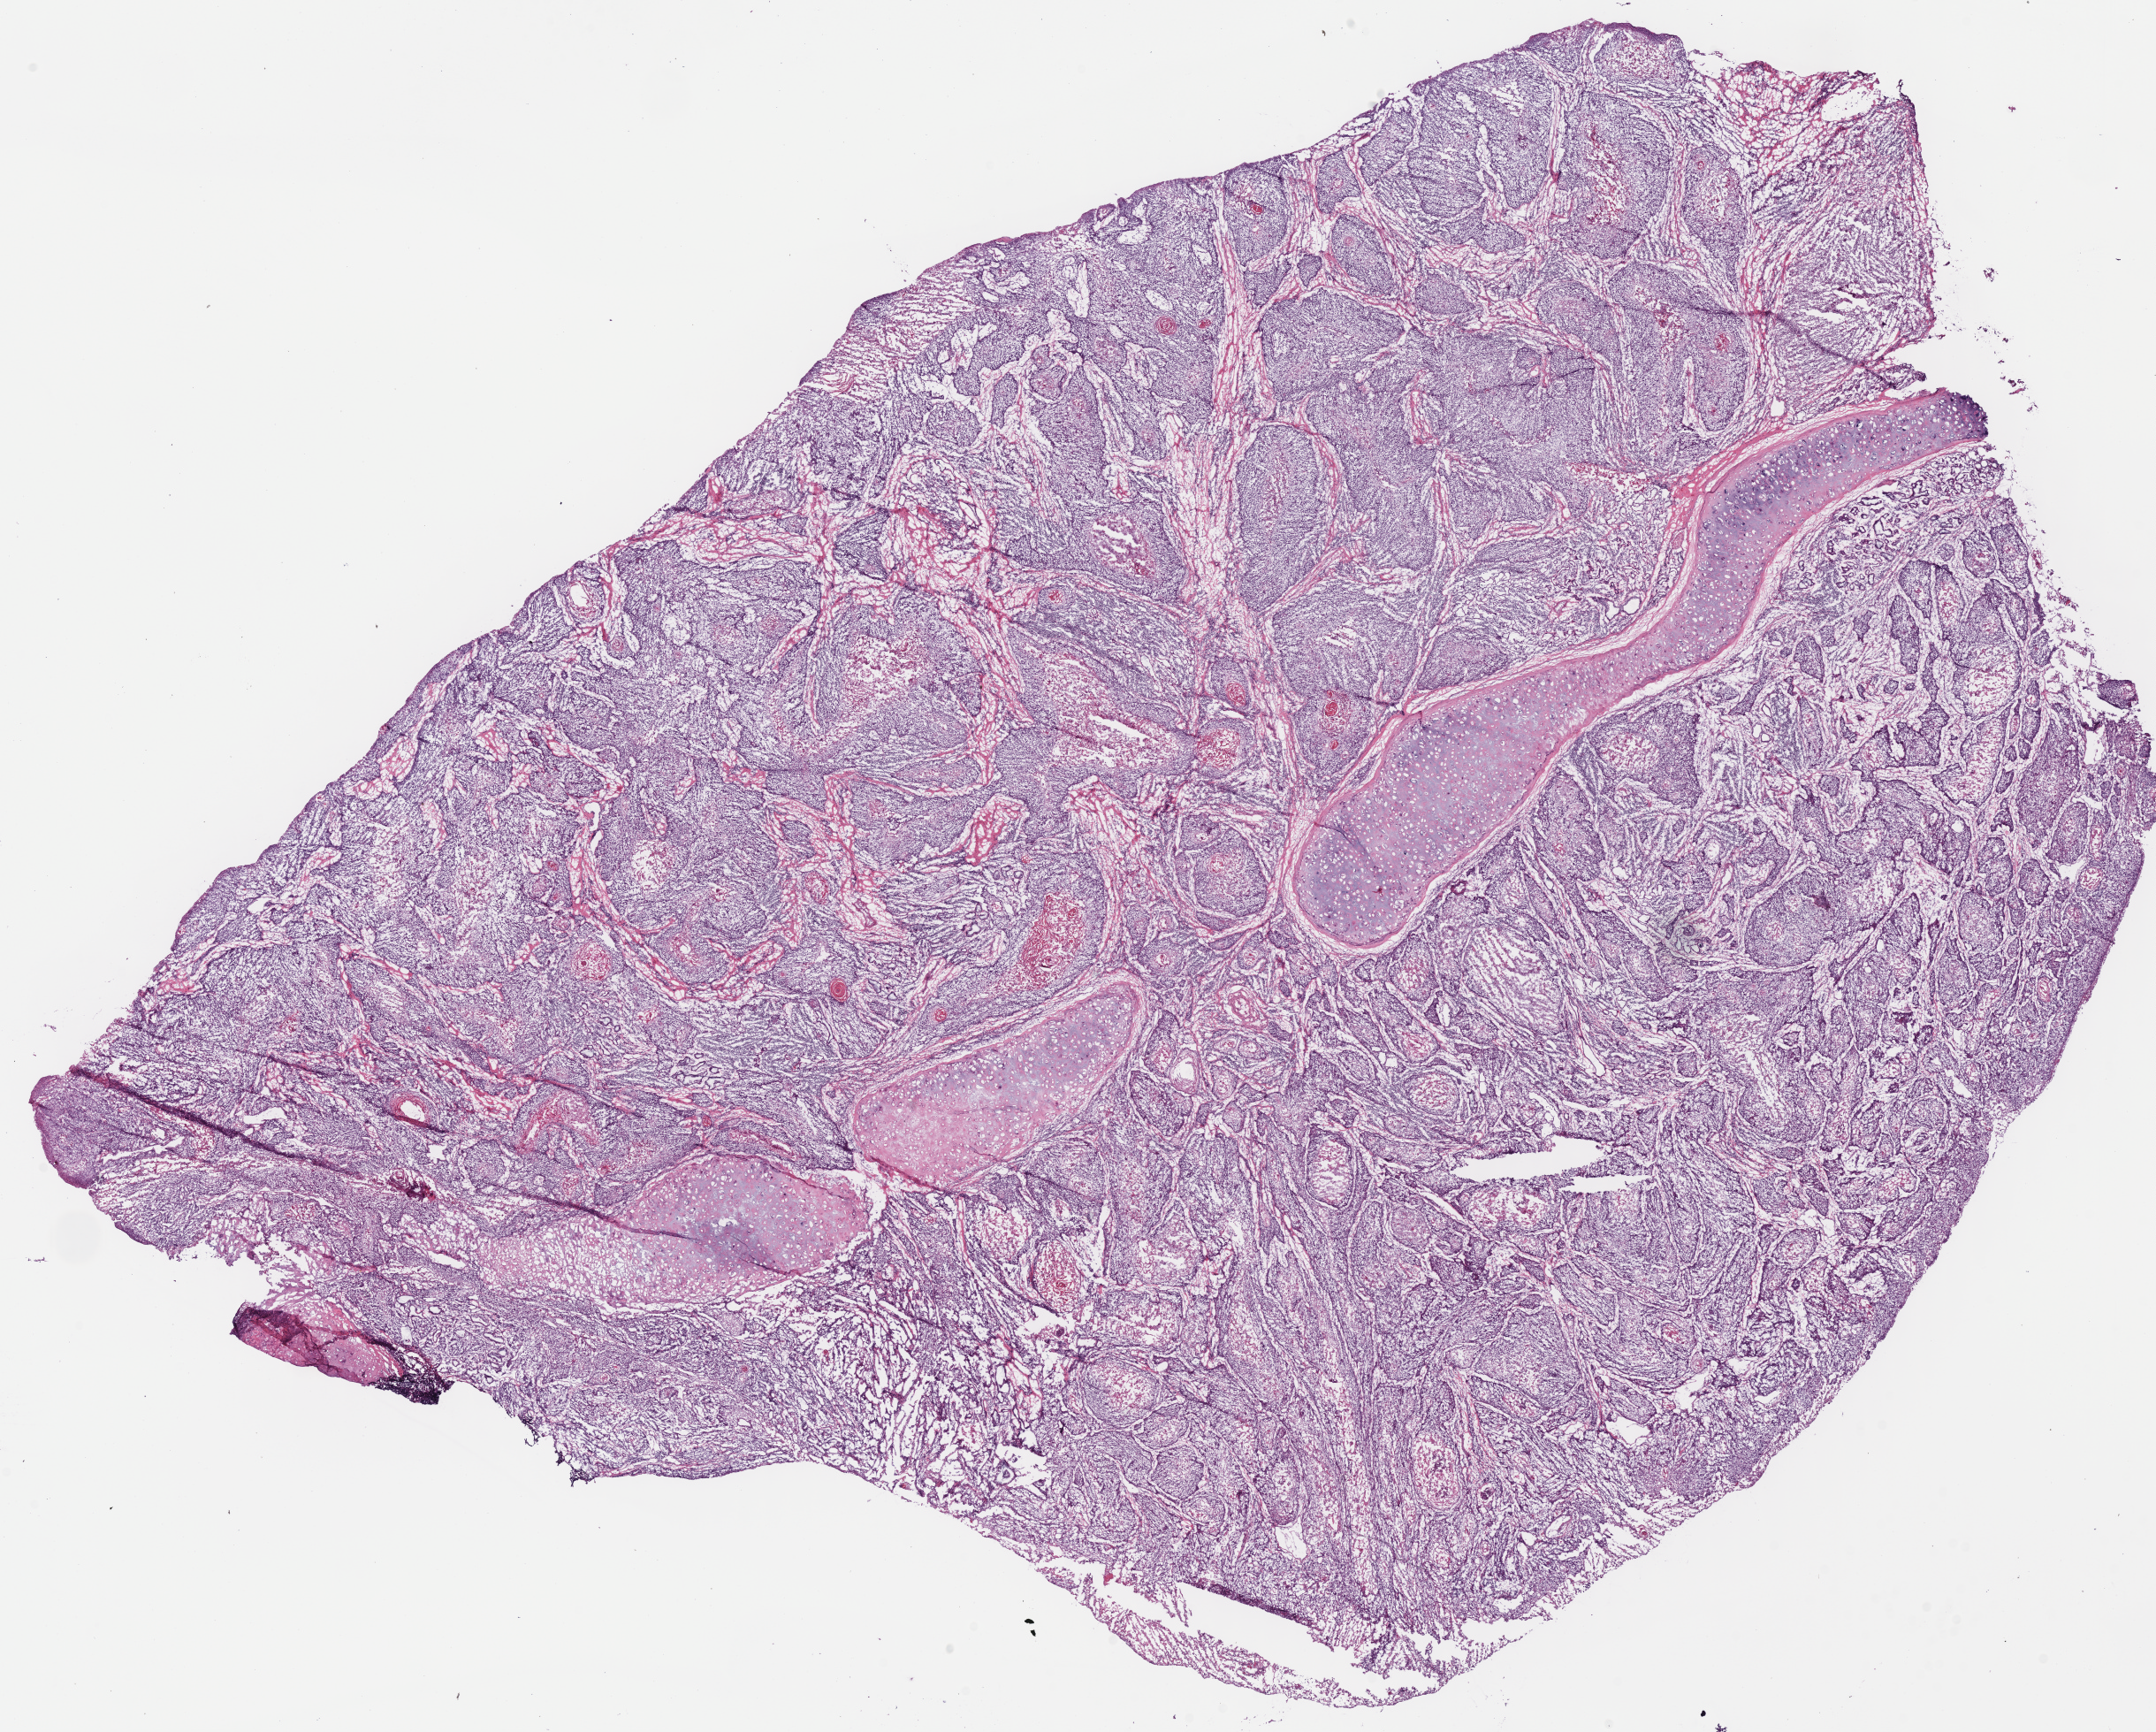
Whole-slide histology image, Hematoxylin and eosin (H&E) stained, shown as a low-resolution overview of the whole scanned area (about 19.2 x 15.4 mm). Frozen section from the bottom of the tissue portion. Head and neck, primary tumour sample. Male, age 47 years at initial diagnosis.
Diagnosis: Squamous cell carcinoma, NOS (larynx, NOS).